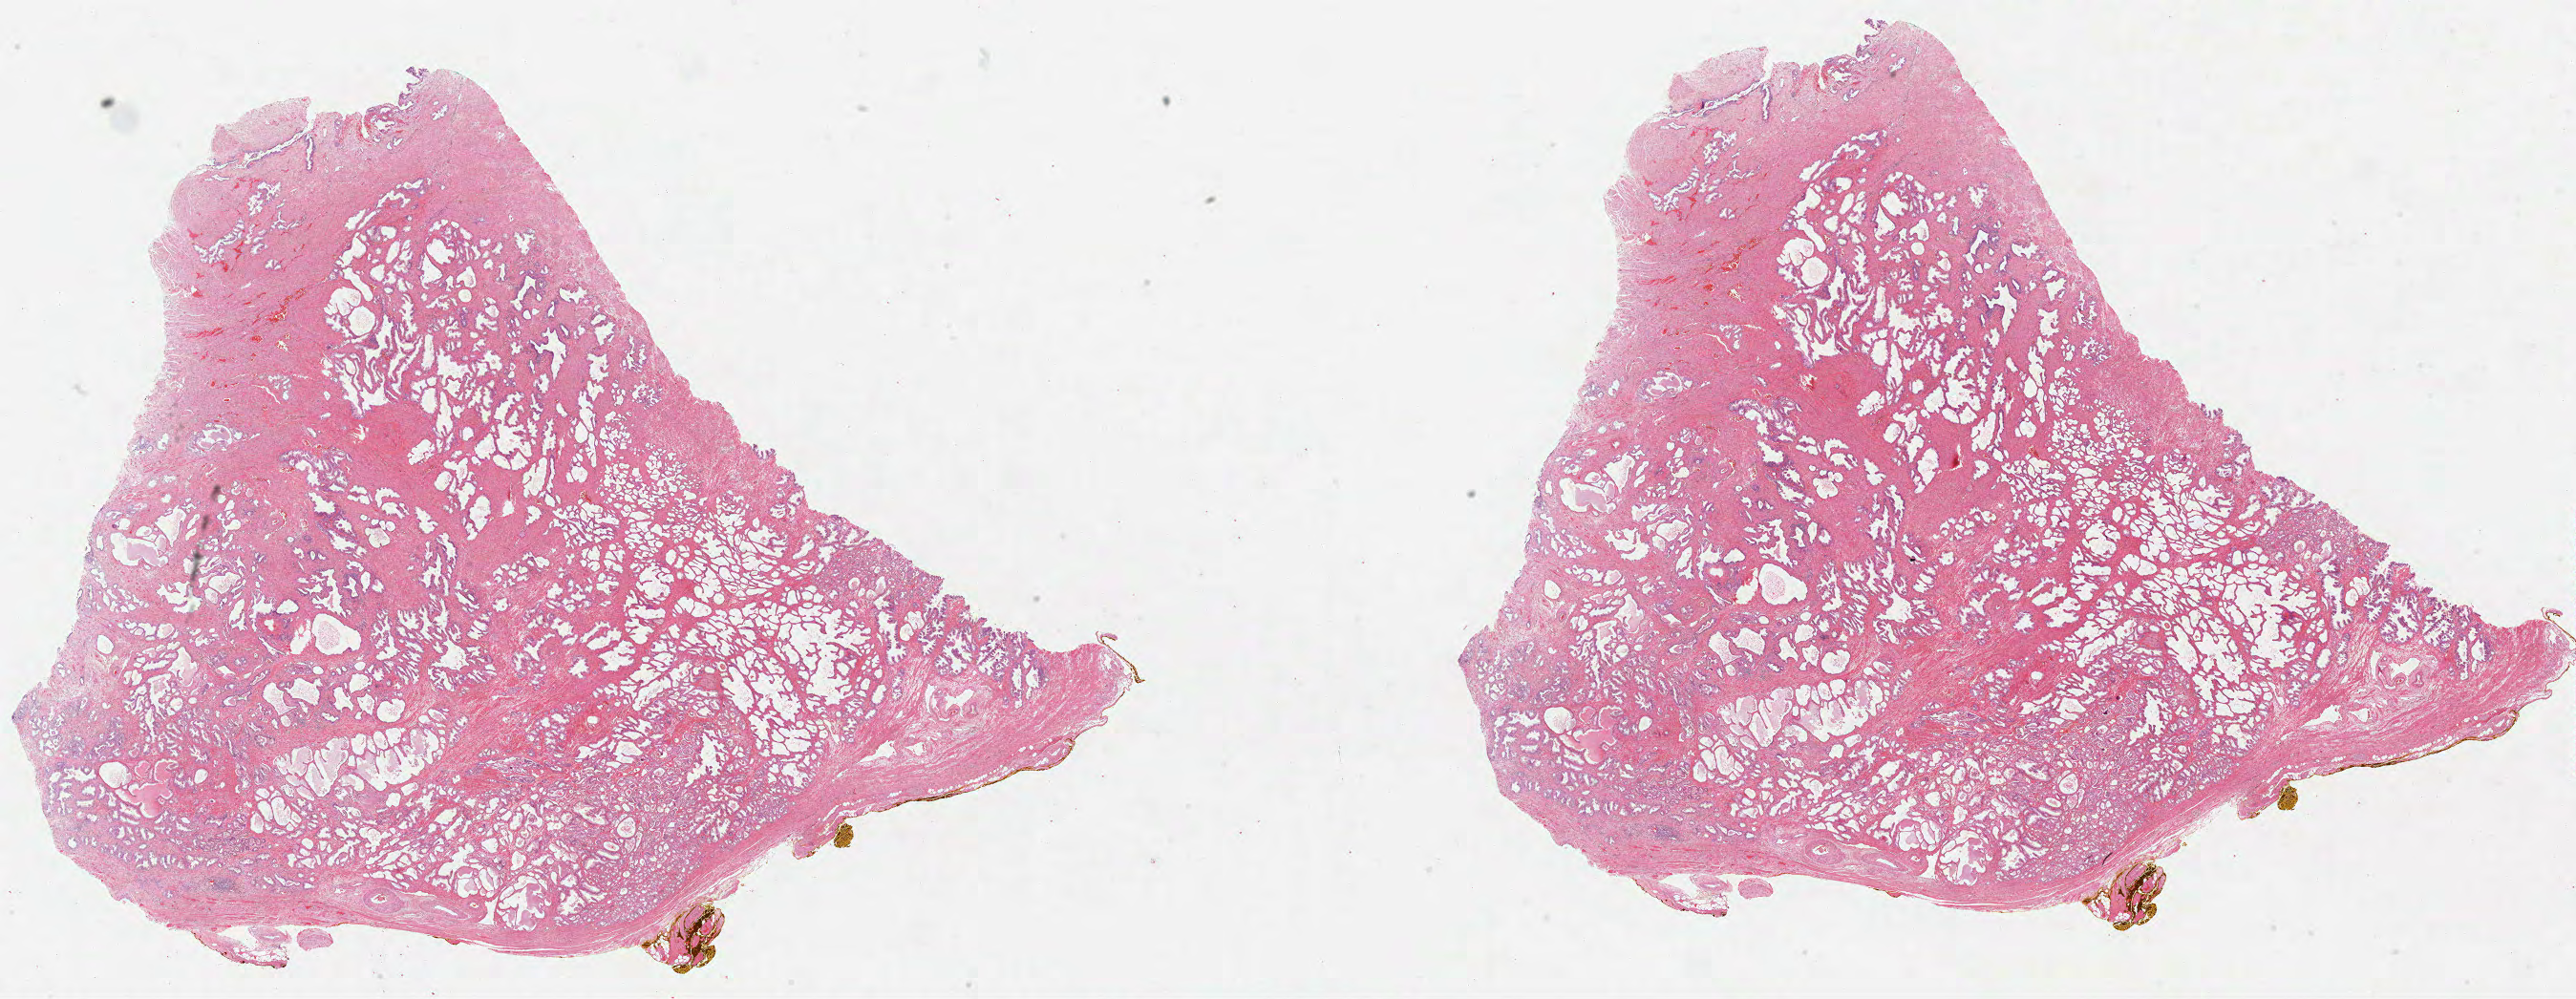
Digitized Hematoxylin and eosin (H&E) stained tissue section (whole slide) — low-resolution overview of the scanned area, about 43.5 x 16.9 mm. Formalin-fixed paraffin-embedded (FFPE) diagnostic section. Primary tumour sample from the prostate. Male, age 66 years at initial diagnosis.
Histologic diagnosis: Acinar cell carcinoma (prostate gland).